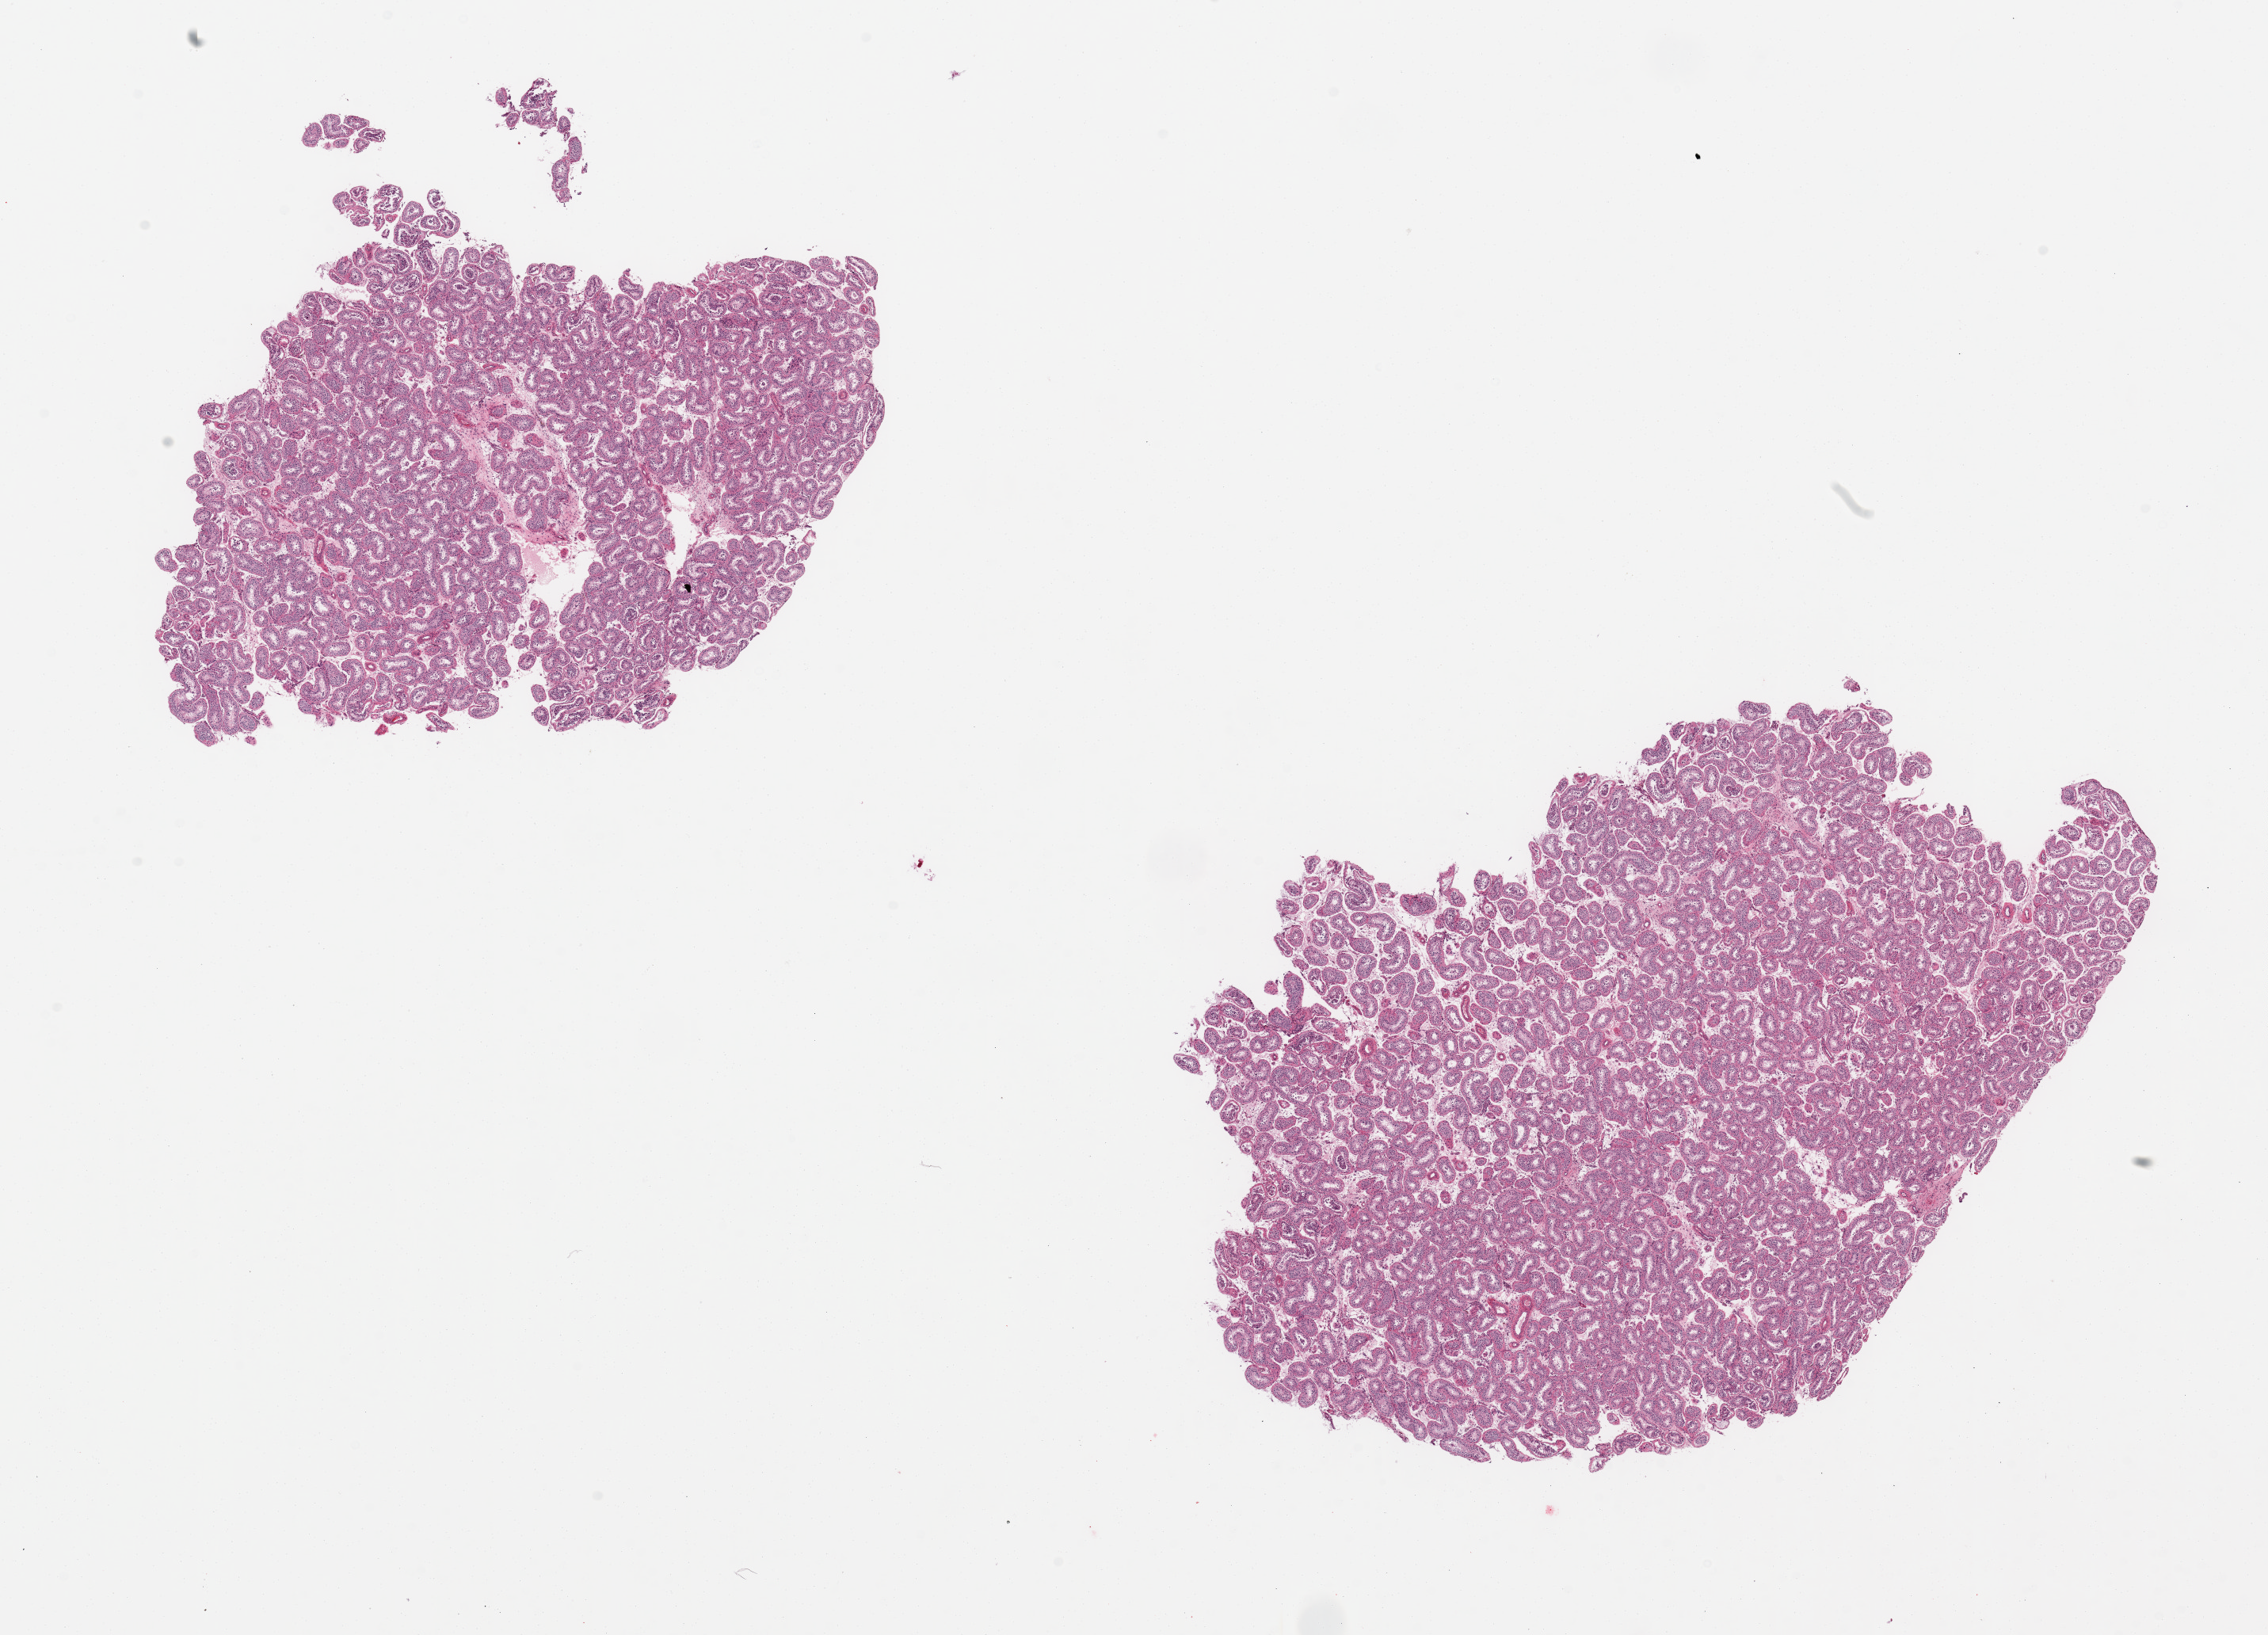
Digitized hematoxylin and eosin (H&E)-stained section — whole scanned area (about 22.6 x 16.3 mm) shown as a low-resolution overview. PAXgene-fixed, paraffin-embedded tissue. Sampled site (target tissue): testis. Tissue donor sample.
Review note (as recorded): 2 pieces; decreased sperm maturation.